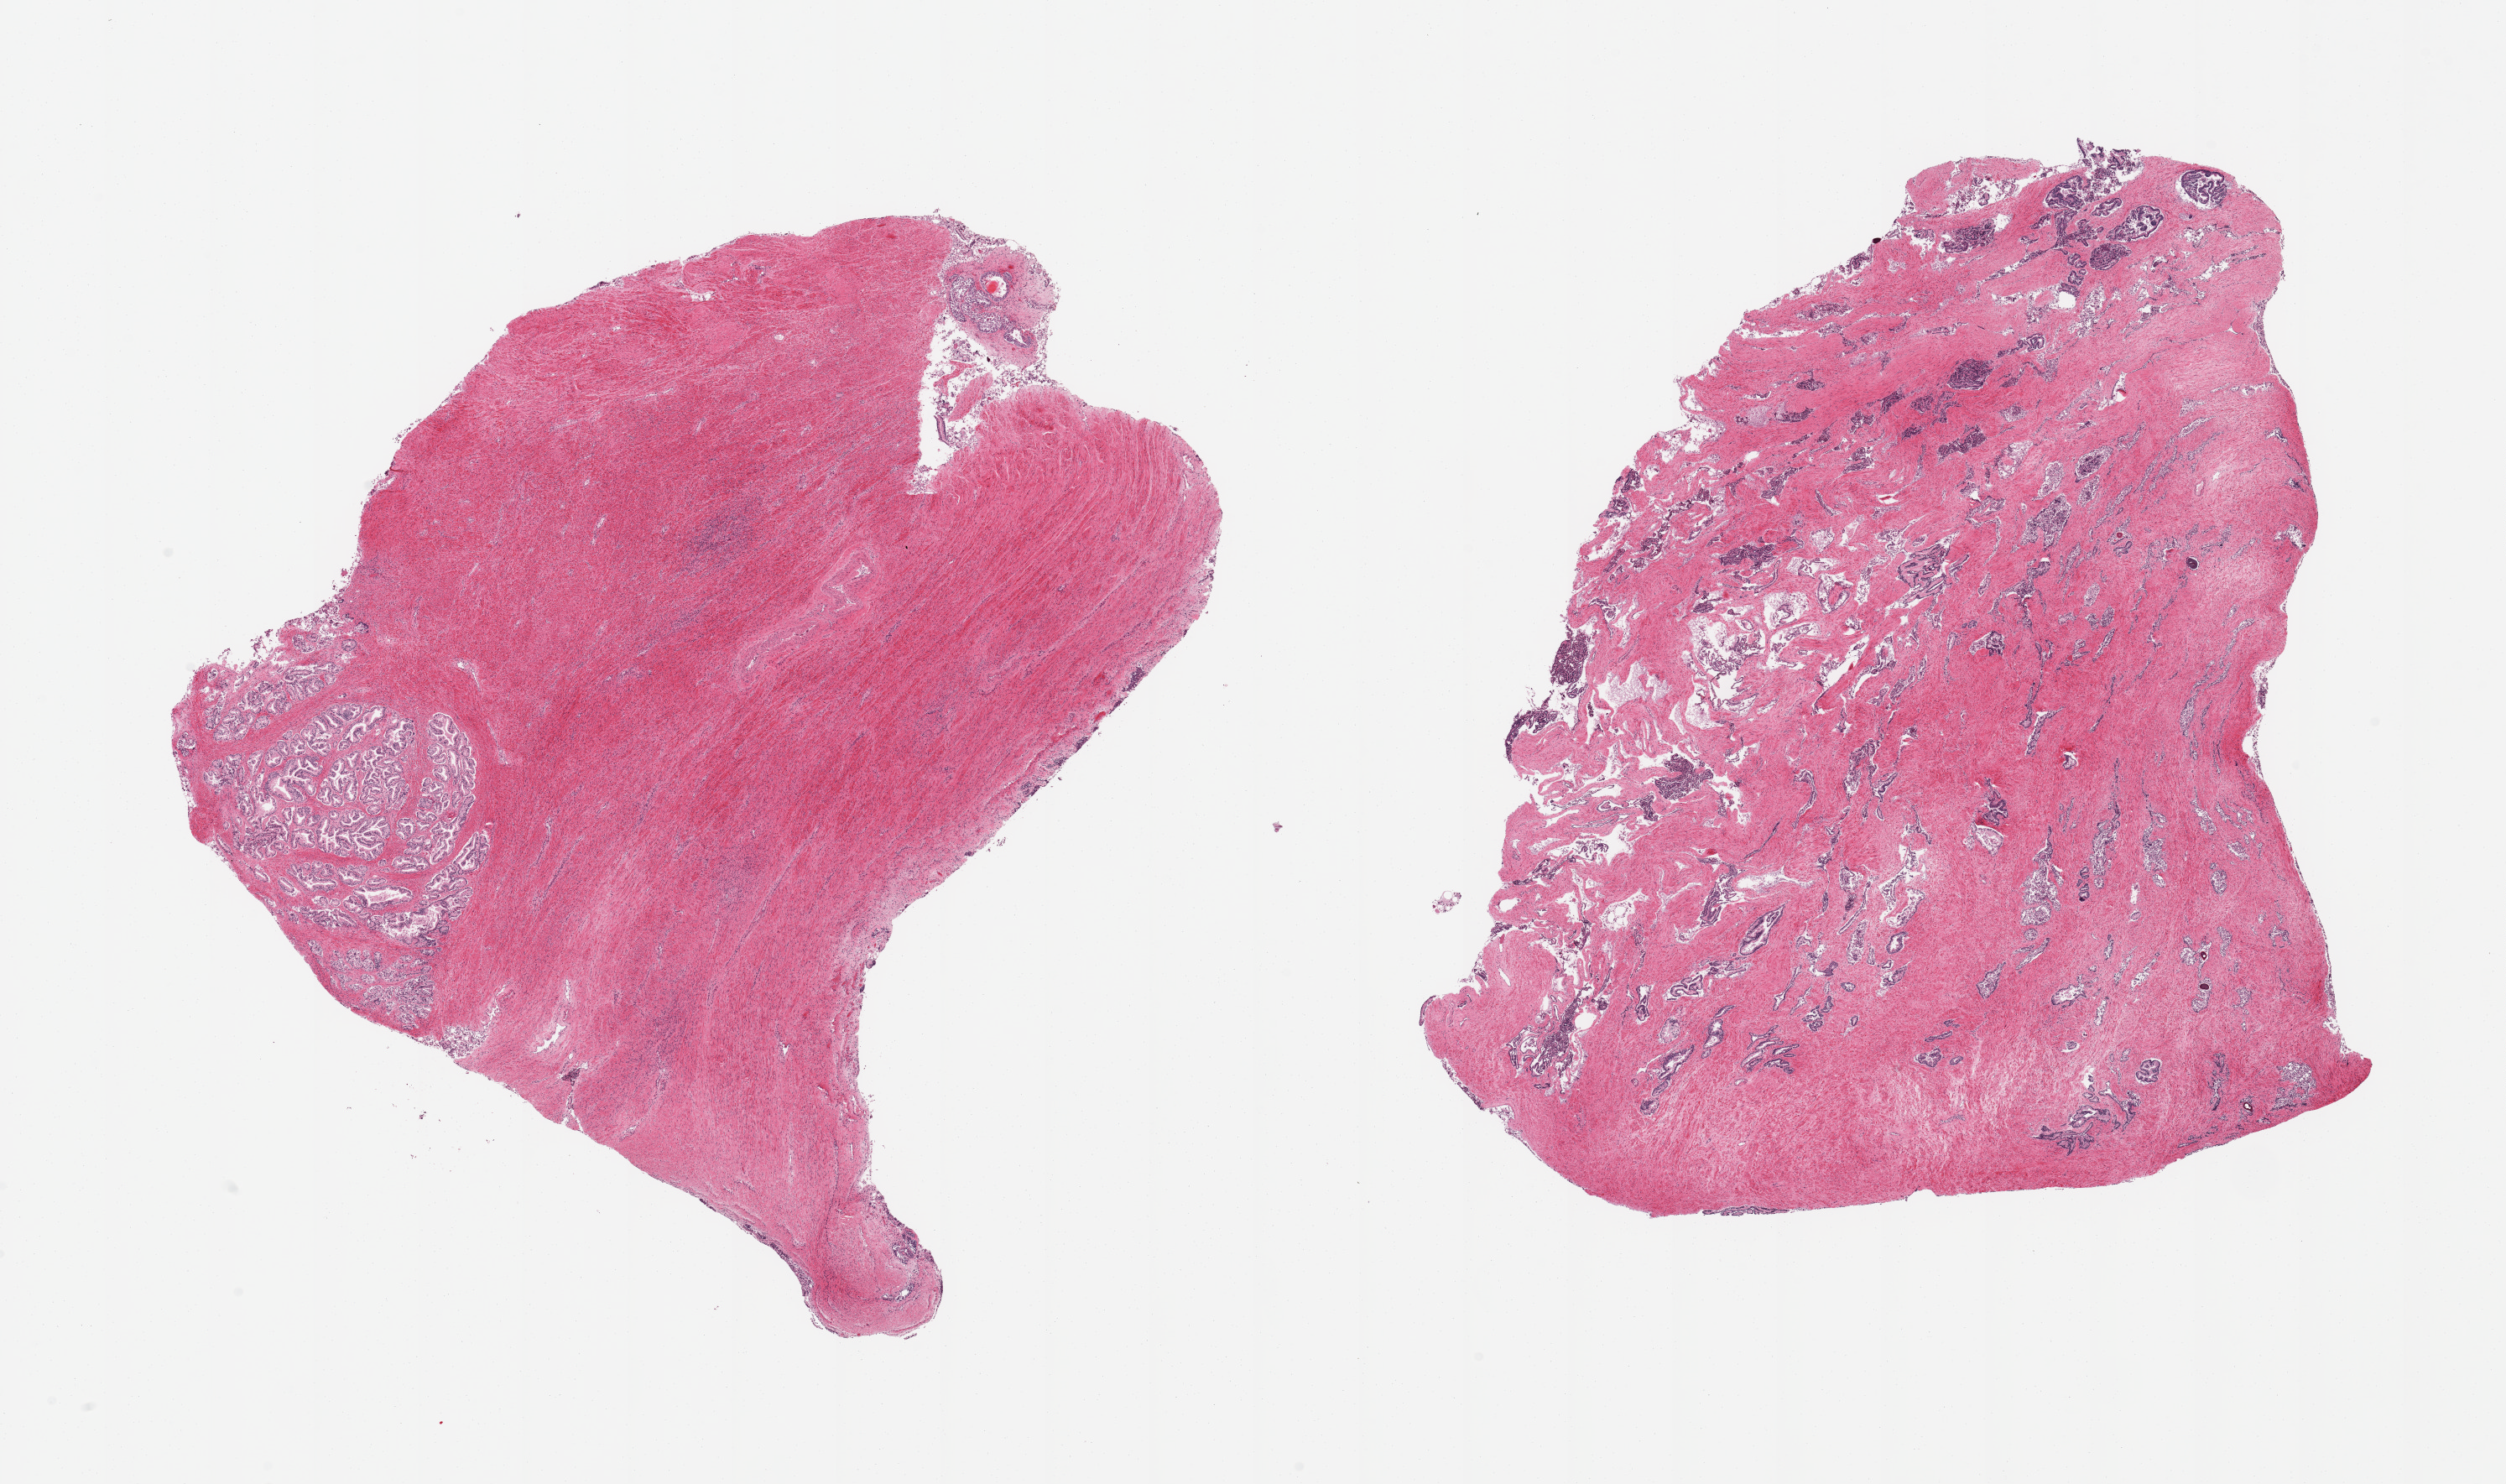
Digitized hematoxylin and eosin (H&E)-stained section — whole scanned area (about 23.6 x 14.0 mm, from a 20x scan) shown as a low-resolution overview, PAXgene-fixed, paraffin-embedded tissue, target tissue: prostate, donor tissue sample.
Reviewer comment on this tissue sample: 2 pieces; one focus of remarkably well-preserved glands, rest with moderately-advanced autolysis, hyperplastic glandular pattern.